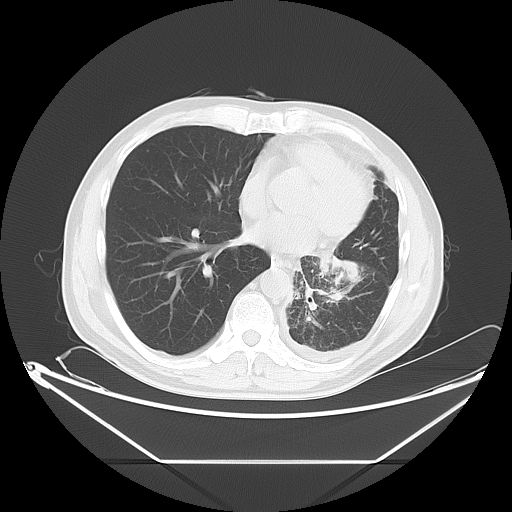
Chest CT, one axial slice. Position 27 of 63 along the scan axis. Reconstruction kernel LUNG. Lung window (W 1500 / L -600 HU). 5 mm slice thickness. 512 × 512 image matrix, field of view 442 × 442 mm. Male patient, age 60 years. Case-level facts recorded for this patient, not image findings: clinical TNM (as recorded): T4 N1 M1.
Outlined on this slice (bounding box drawn by a radiologist):
- lung tumour (recorded histology: adenocarcinoma): bounding box (x1, y1, x2, y2) in pixels: (315, 250, 375, 312)